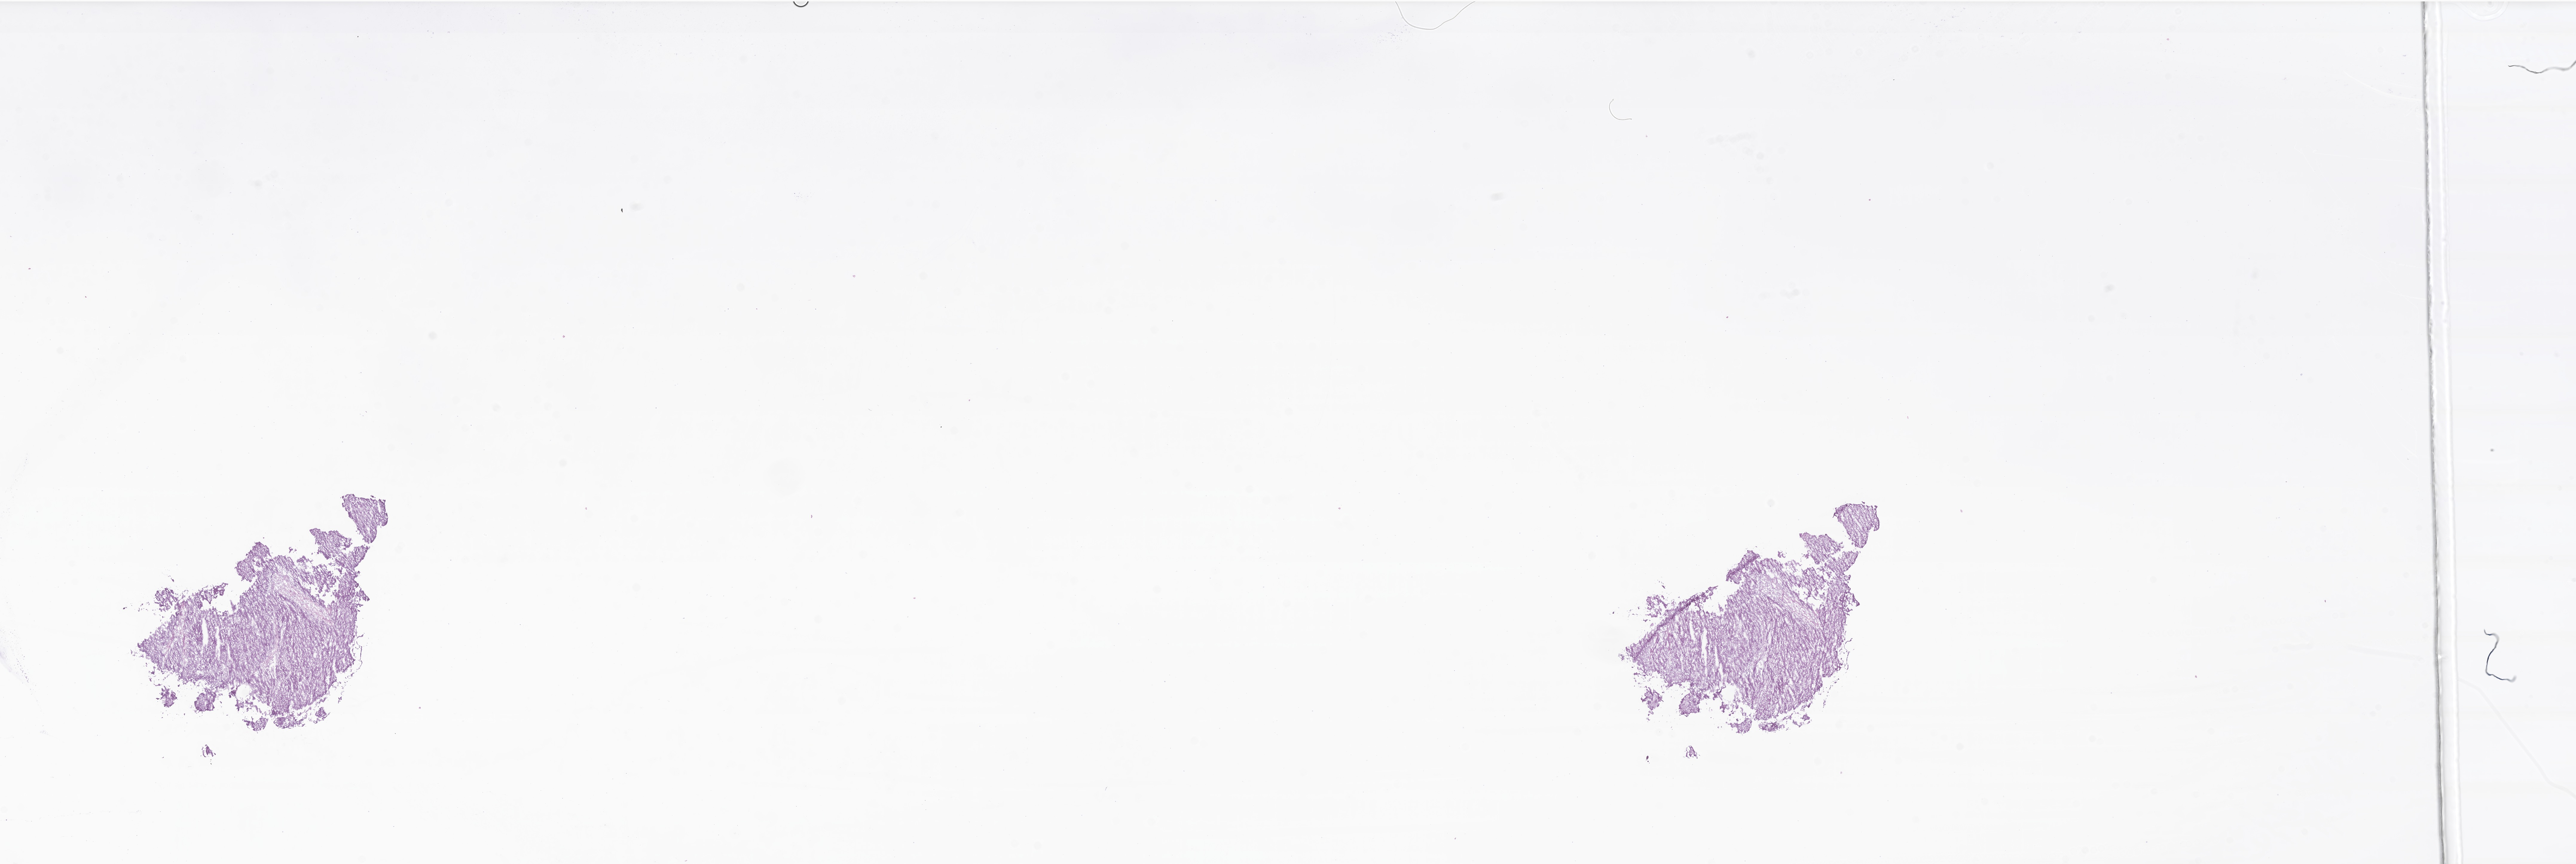
Digitized haematoxylin and eosin-stained section of tumor tissue from the adrenal gland, whole scanned area (about 36.3 x 12.2 mm) shown as a low-resolution overview; frozen section. Female patient, age 657 days.
* diagnosis: Adrenal cortical carcinoma